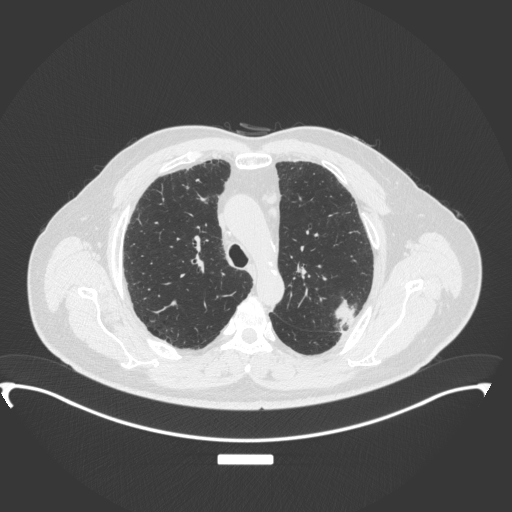
Chest CT, one axial slice. Slice 258 of 350 in the series (ordered by position). Reconstruction kernel B31f. Lung window (W 1500 / L -600 HU). 1 mm slice thickness. 512 × 512 image matrix, field of view 459 × 459 mm. Patient: male, 64 years. Case-level facts recorded for this patient, not image findings: clinical TNM (as recorded): T1c N1 M1.
Outlined on this slice (bounding box drawn by a radiologist):
- lung tumour (recorded histology: adenocarcinoma): bounding box <333,294,358,330> (left, top, right, bottom; pixels)